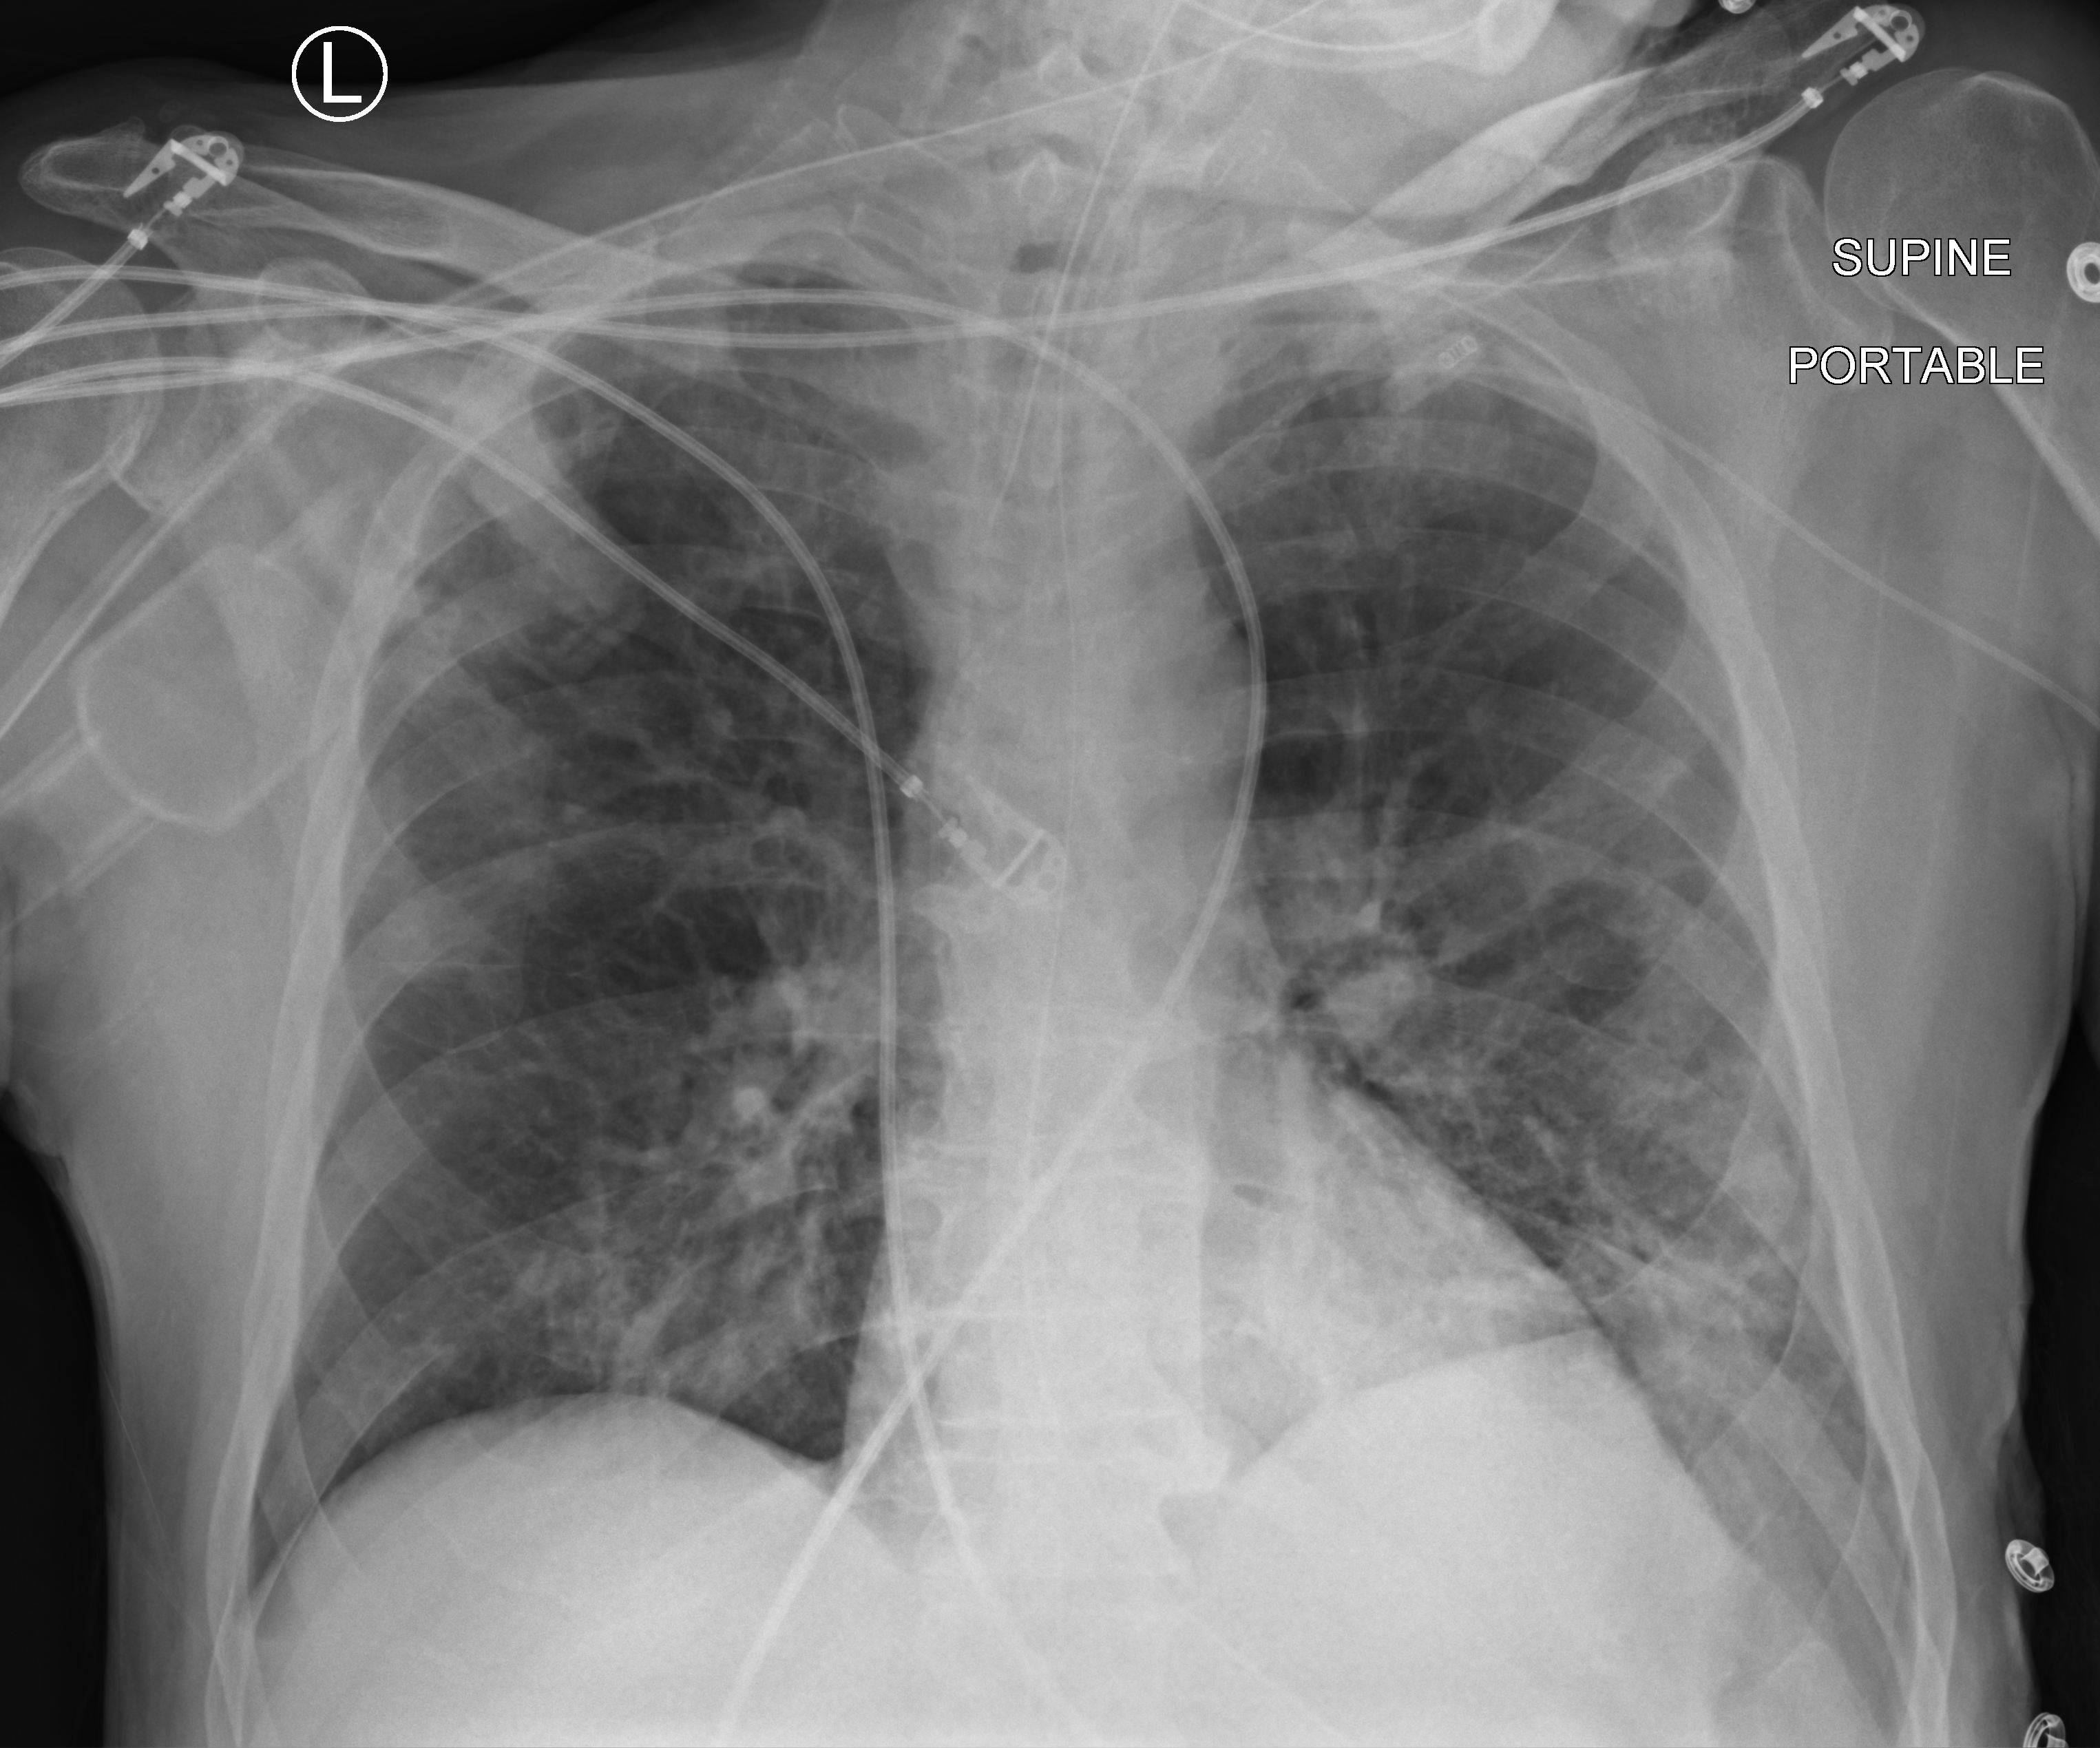
Portable chest radiograph, anteroposterior (AP) projection. Patient hospitalised with COVID-19; male, aged 60–74 years.
From the hospital-stay record, not from the radiograph (when in the stay this image was taken is not recorded): chronic kidney disease (admission record): no; COPD (admission record): no; hypertension (admission record): yes.